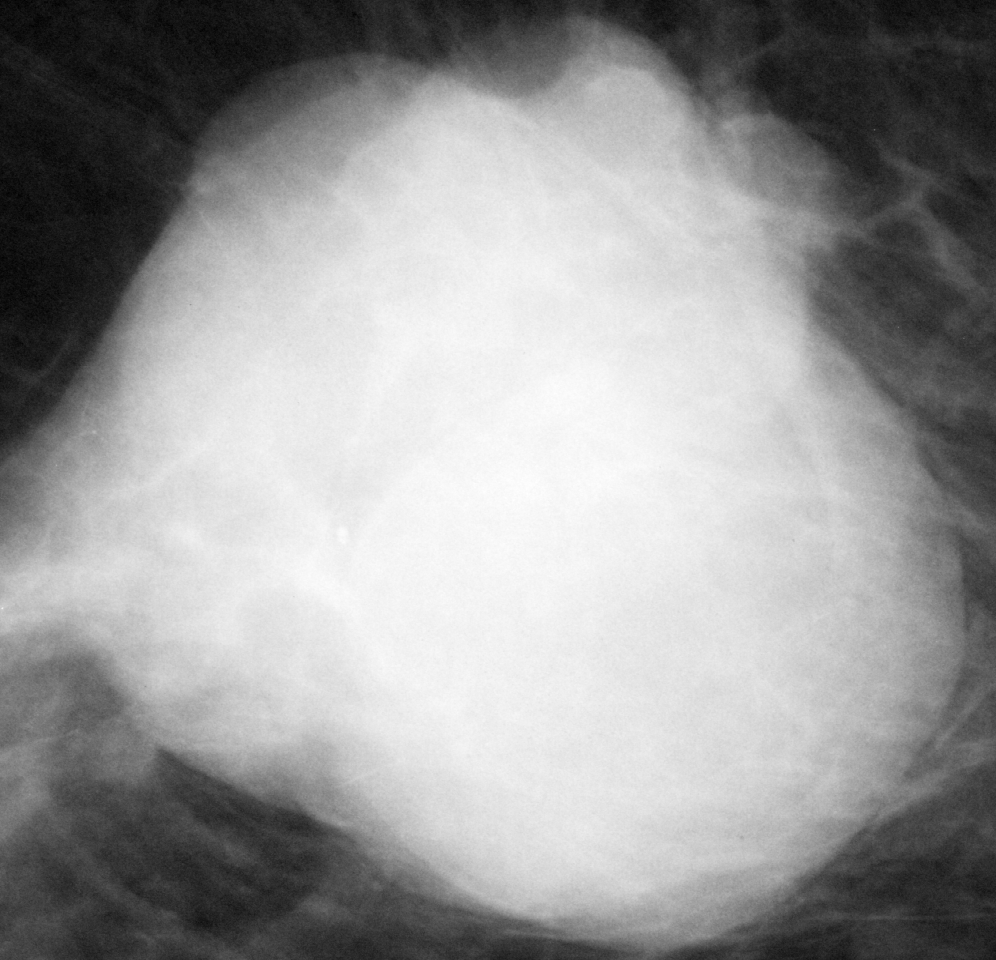
Region of interest cut from a scanned film mammogram (one marked finding), right breast, CC view.
- Mass, shape lobulated, margins circumscribed; BI-RADS assessment category 5; subtlety rating 5 on a 1 (subtle) to 5 (obvious) scale; pathology result (as recorded, not read from the image): malignant.